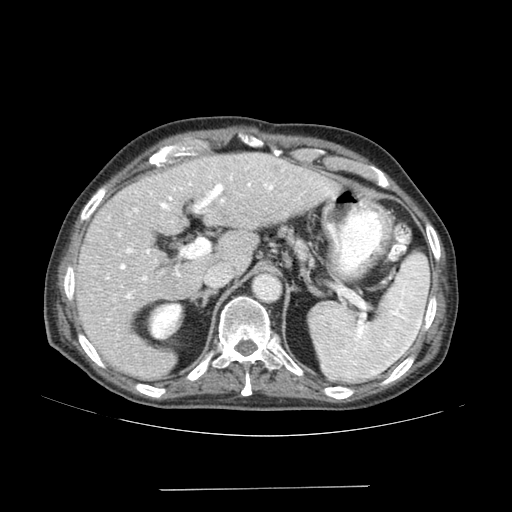
Contrast-enhanced abdominal CT (liver protocol), one axial slice; position 108 of 192 along the scan axis; reconstruction kernel SOFT; 120 kVp; soft-tissue window (W 400 / L 40 HU); 2.5 mm slice thickness; 512 × 512 image matrix, field of view 400 × 400 mm. Case-level facts recorded for this patient, not image findings: diagnosis: hepatocellular carcinoma (patient treated with transarterial chemoembolisation; whether this scan precedes or follows treatment is not stated here); TNM stage (as recorded): Stage-IVA; Child-Pugh class: A; tumour differentiation: poorly differentiated.
Structures marked on this image (semi-automatically segmented with operator editing):
- liver parenchyma outside the tumour (the mass and vessels are separate outlines, so this box may not span the whole liver): bounding box <76,152,338,380> (left, top, right, bottom; pixels)
- liver vessels: <106,168,330,299>